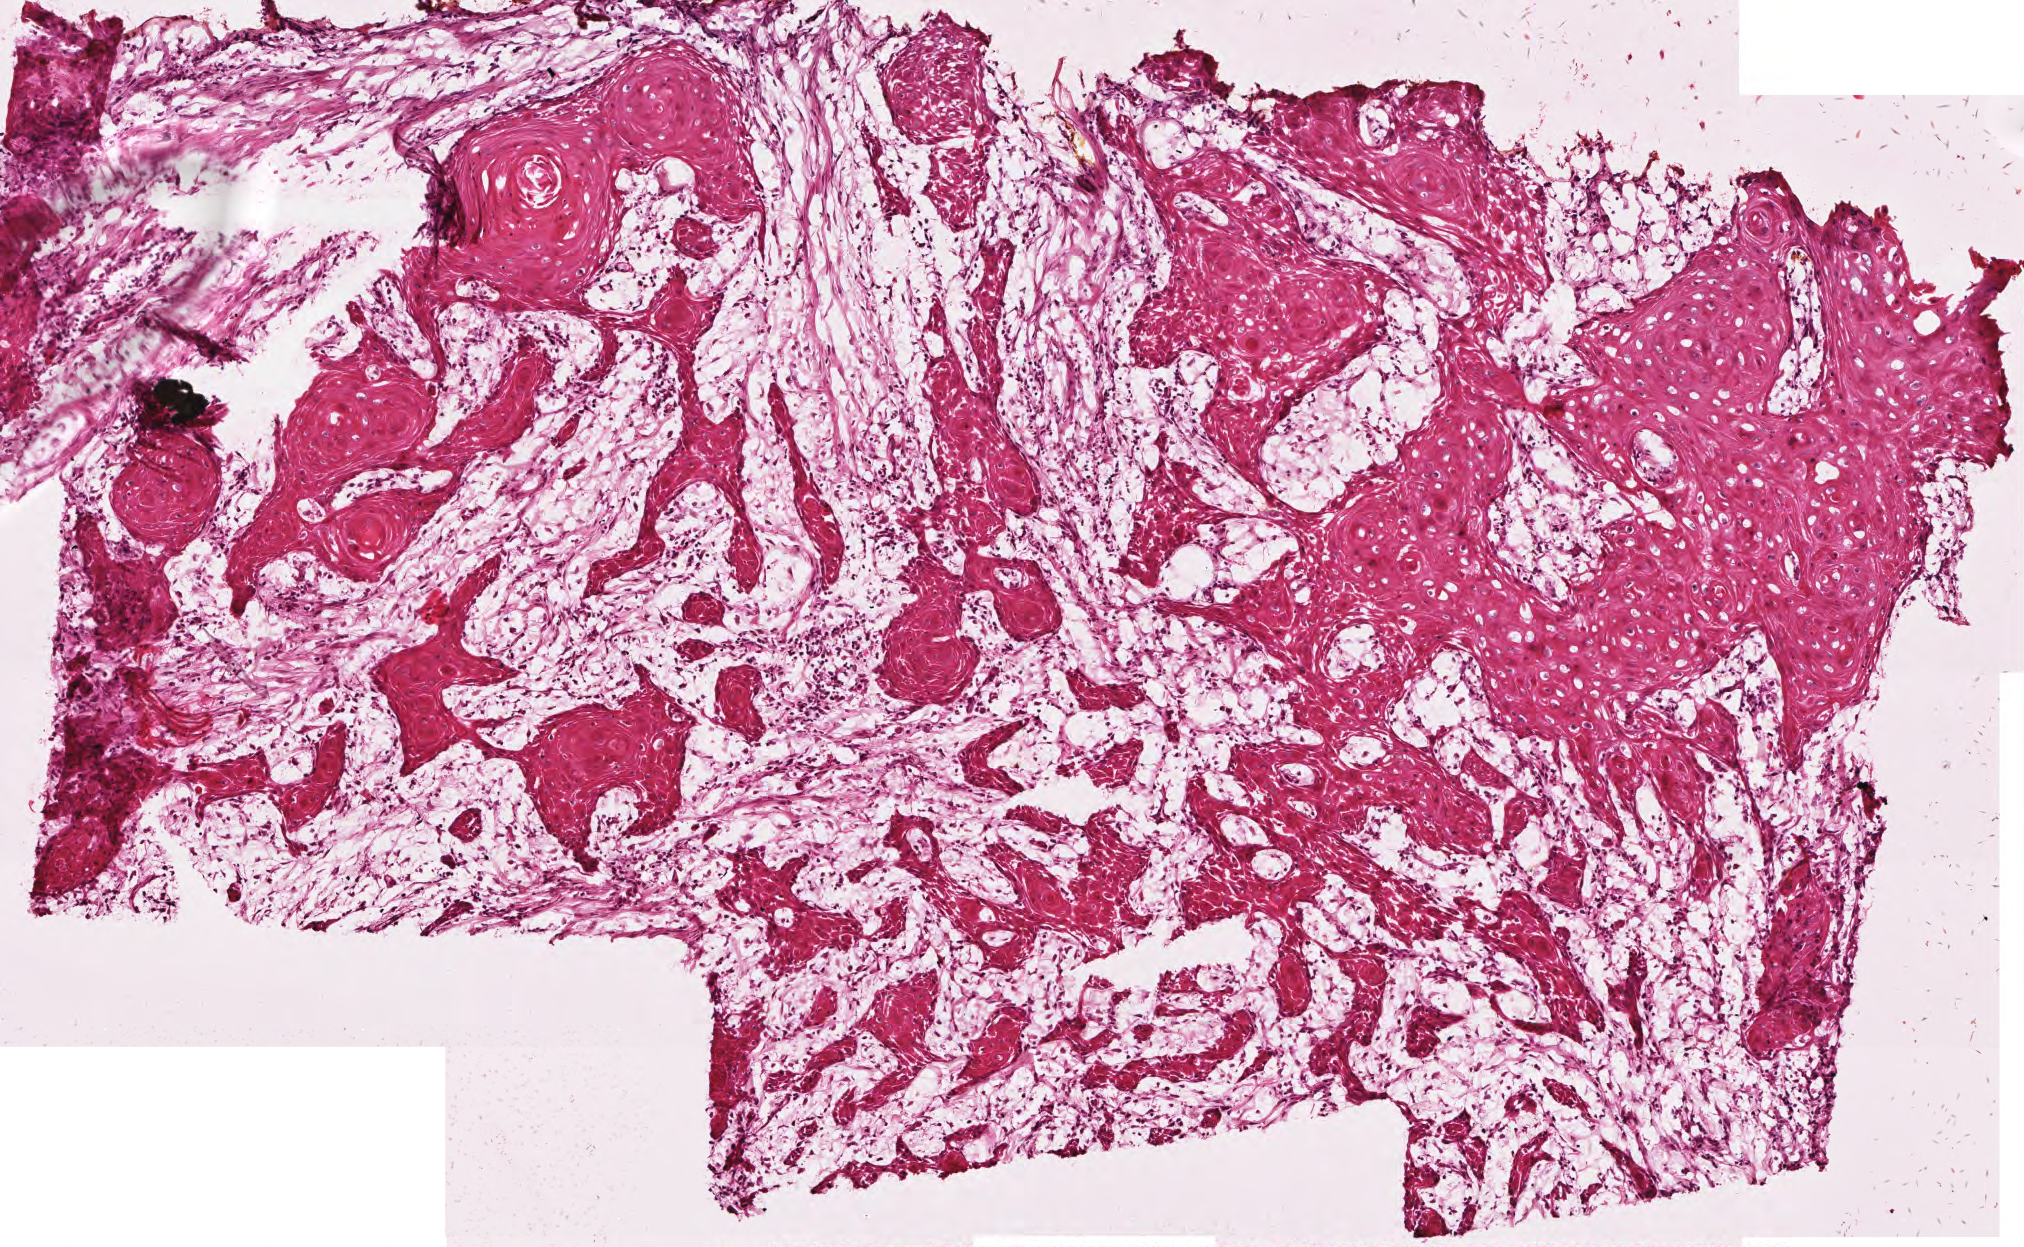
H&E-stained whole-slide image, whole scanned area (about 4.0 x 2.5 mm) shown as a low-resolution overview; frozen section from the top of the tissue portion; sample: primary tumour, head and neck. Male, age 69 years at initial diagnosis. Histologic grade: G1 (well differentiated). Composition of this section per pathologist review: tumour cells 60%, tumour nuclei 65%, normal cells 0%, stromal cells 40%, necrosis 0%.
- histologic diagnosis: Squamous cell carcinoma, NOS
- TNM: T4a N2c M0
- AJCC pathologic stage: IVA (6th edition)